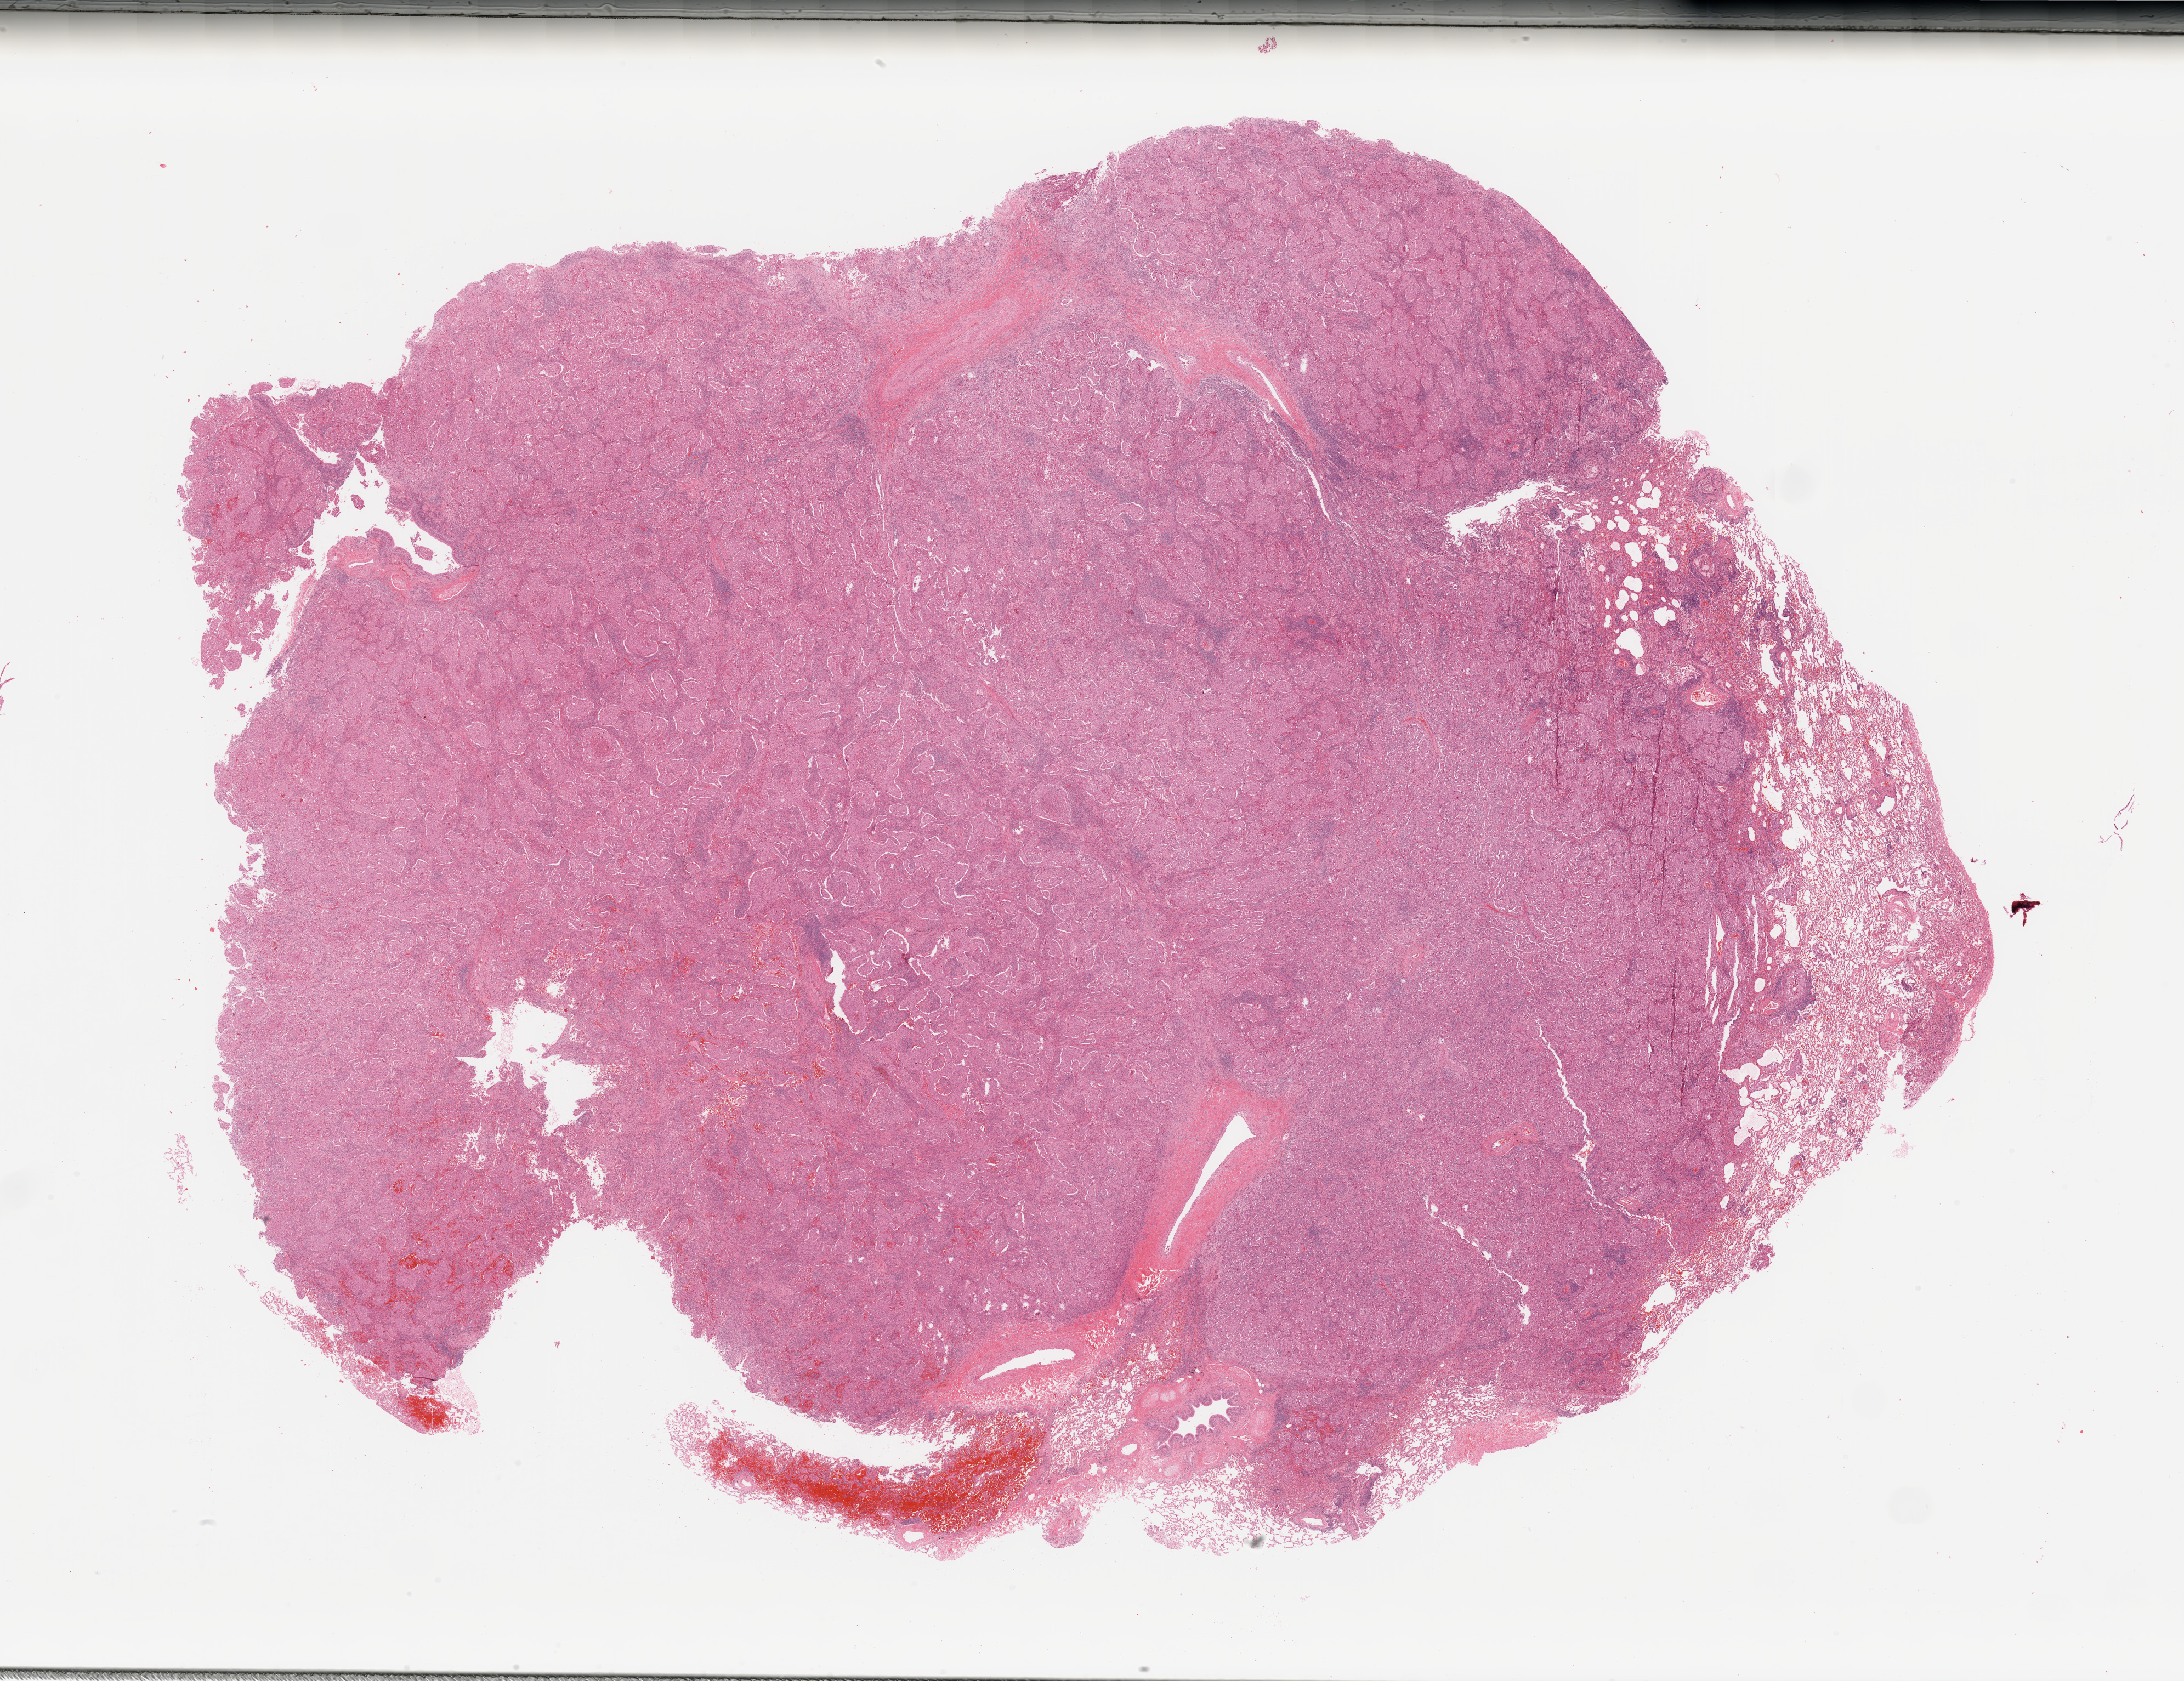
Digitized H&E-stained tissue section (whole slide) — a low-resolution overview of the entire scanned area, about 31.5 x 24.2 mm, tumour tissue sample, lung. Female, 48 y/o.
Histologic diagnosis: Adenocarcinoma, NOS.